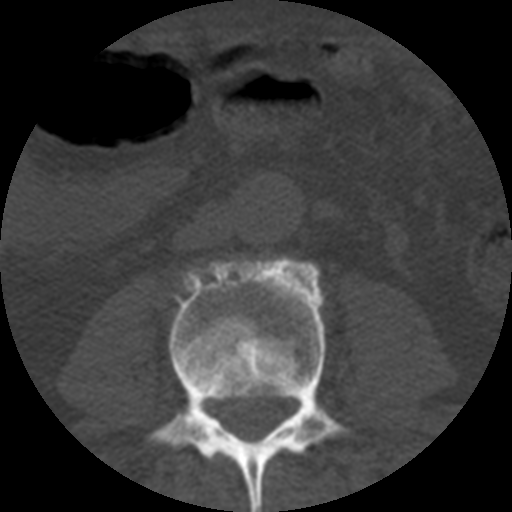
CT including the spine, one axial slice. Position 119 of 508 along the scan axis. 120 kVp. Bone window (W 1800 / L 400 HU). 1.25 mm slice thickness. 512 × 512 image matrix, field of view 160 × 160 mm. Patient age 57 years. Case-level facts recorded for this patient, not image findings: primary cancer: prostate.
Structures marked on this image (semi-automatically segmented with operator editing):
- L2 vertebra: bounding box (x1, y1, x2, y2) in pixels: (274, 446, 284, 453)
- L3 vertebra: (149, 257, 349, 512)